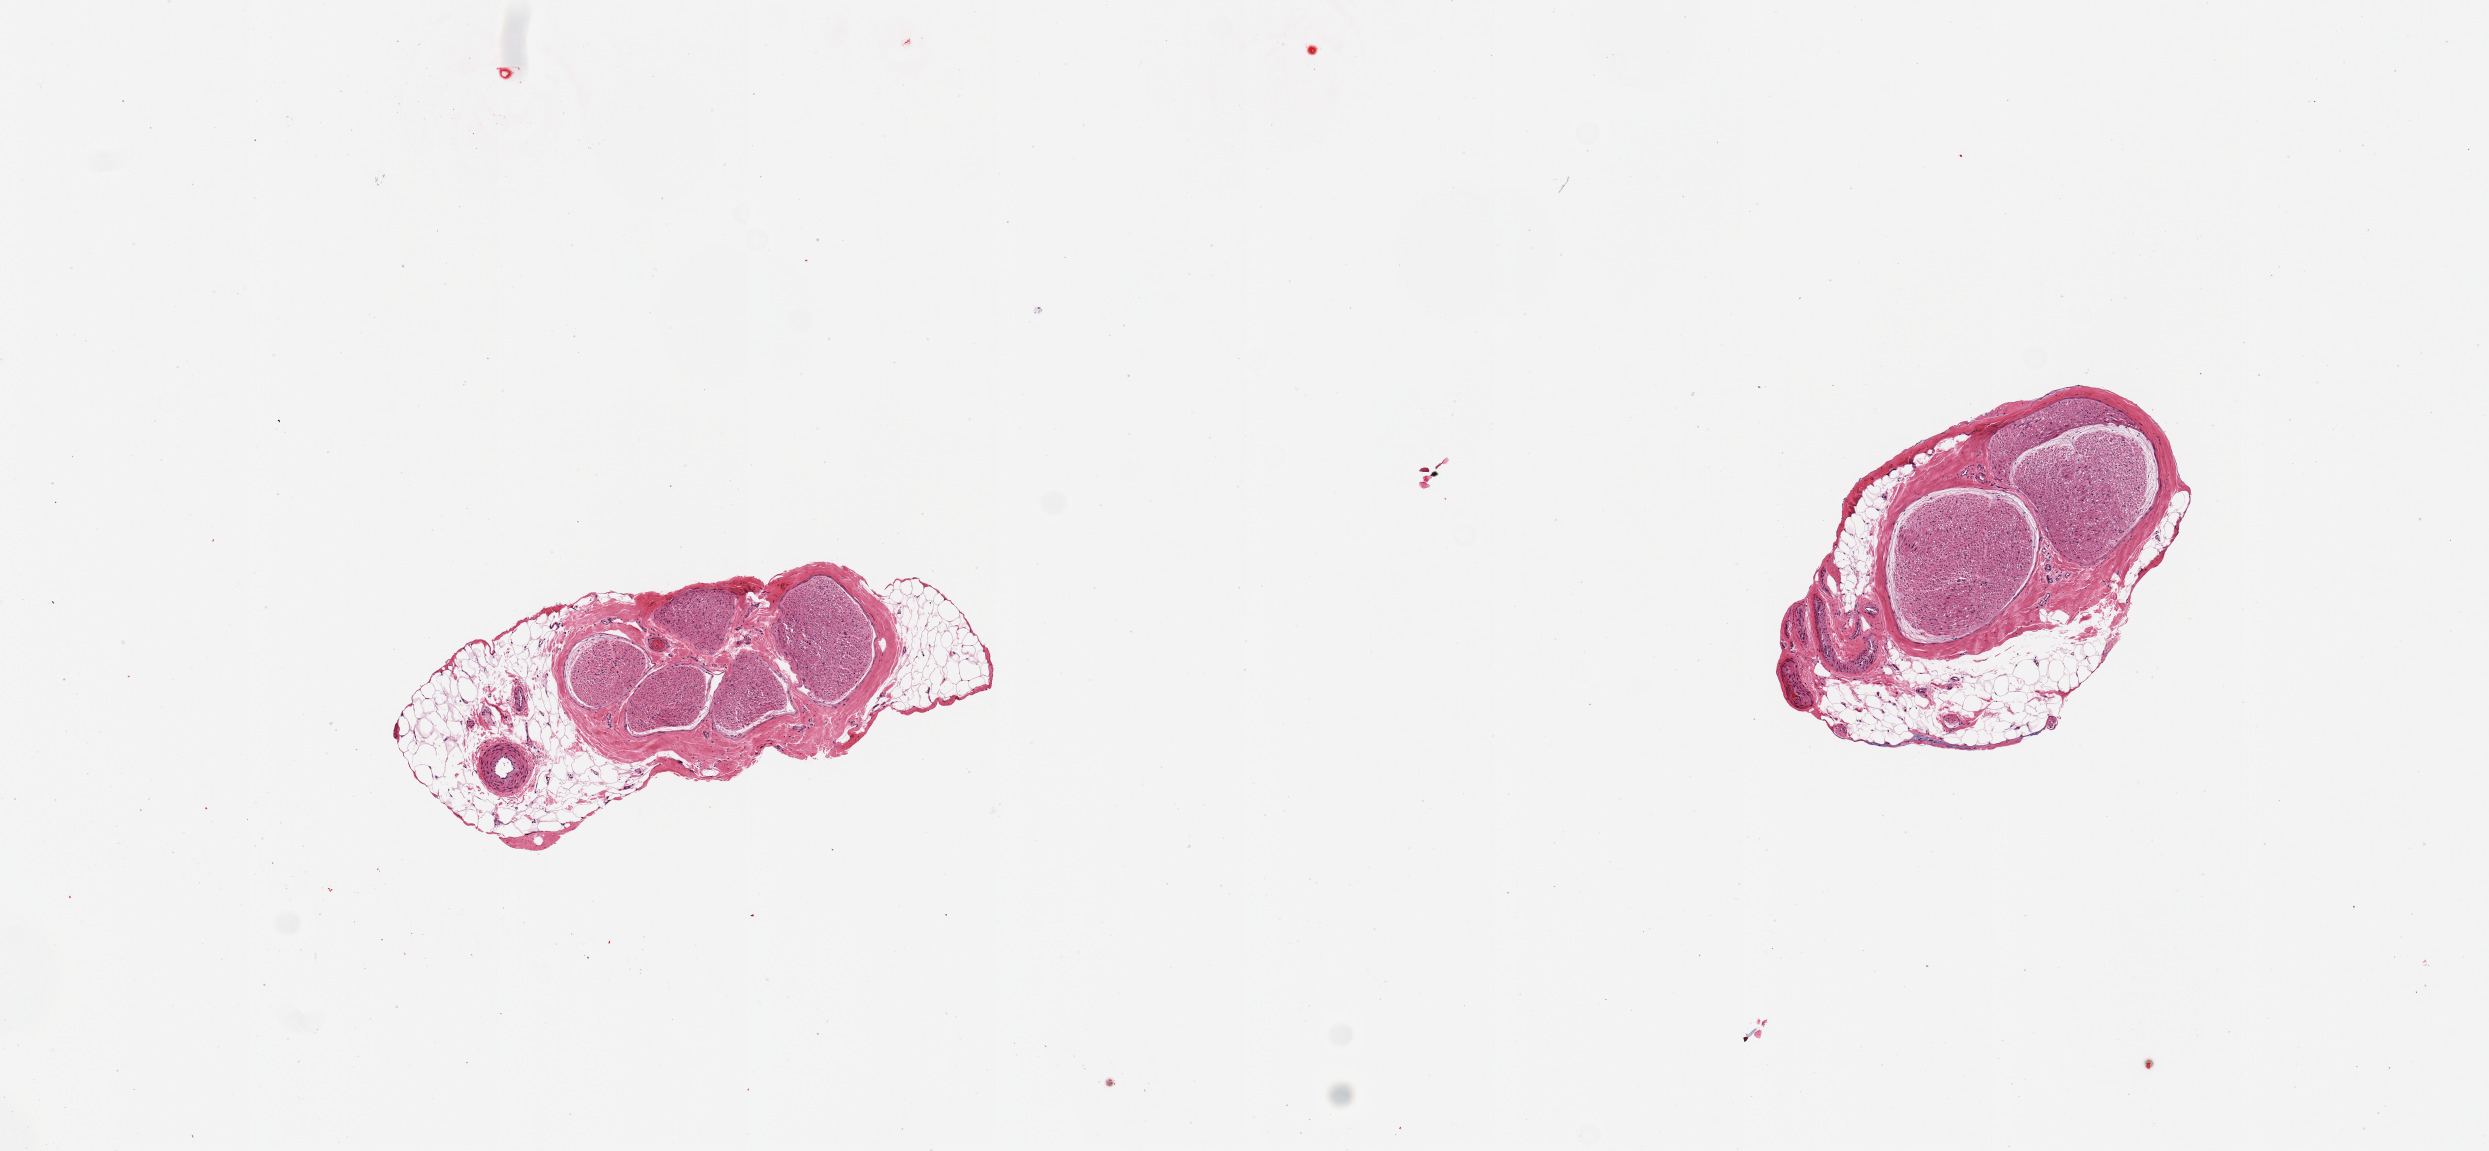
Haematoxylin and eosin whole-slide image, brightfield — low-resolution overview of the scanned area, about 9.8 x 4.6 mm (slide scanned at 20x). PAXgene-fixed, paraffin-embedded tissue. Sampled site (target tissue): tibial nerve. Donor tissue sample. Donor sex: male.
* pathologist's review note for this sample: 2 pieces; external fat 20%; small artery in external fat